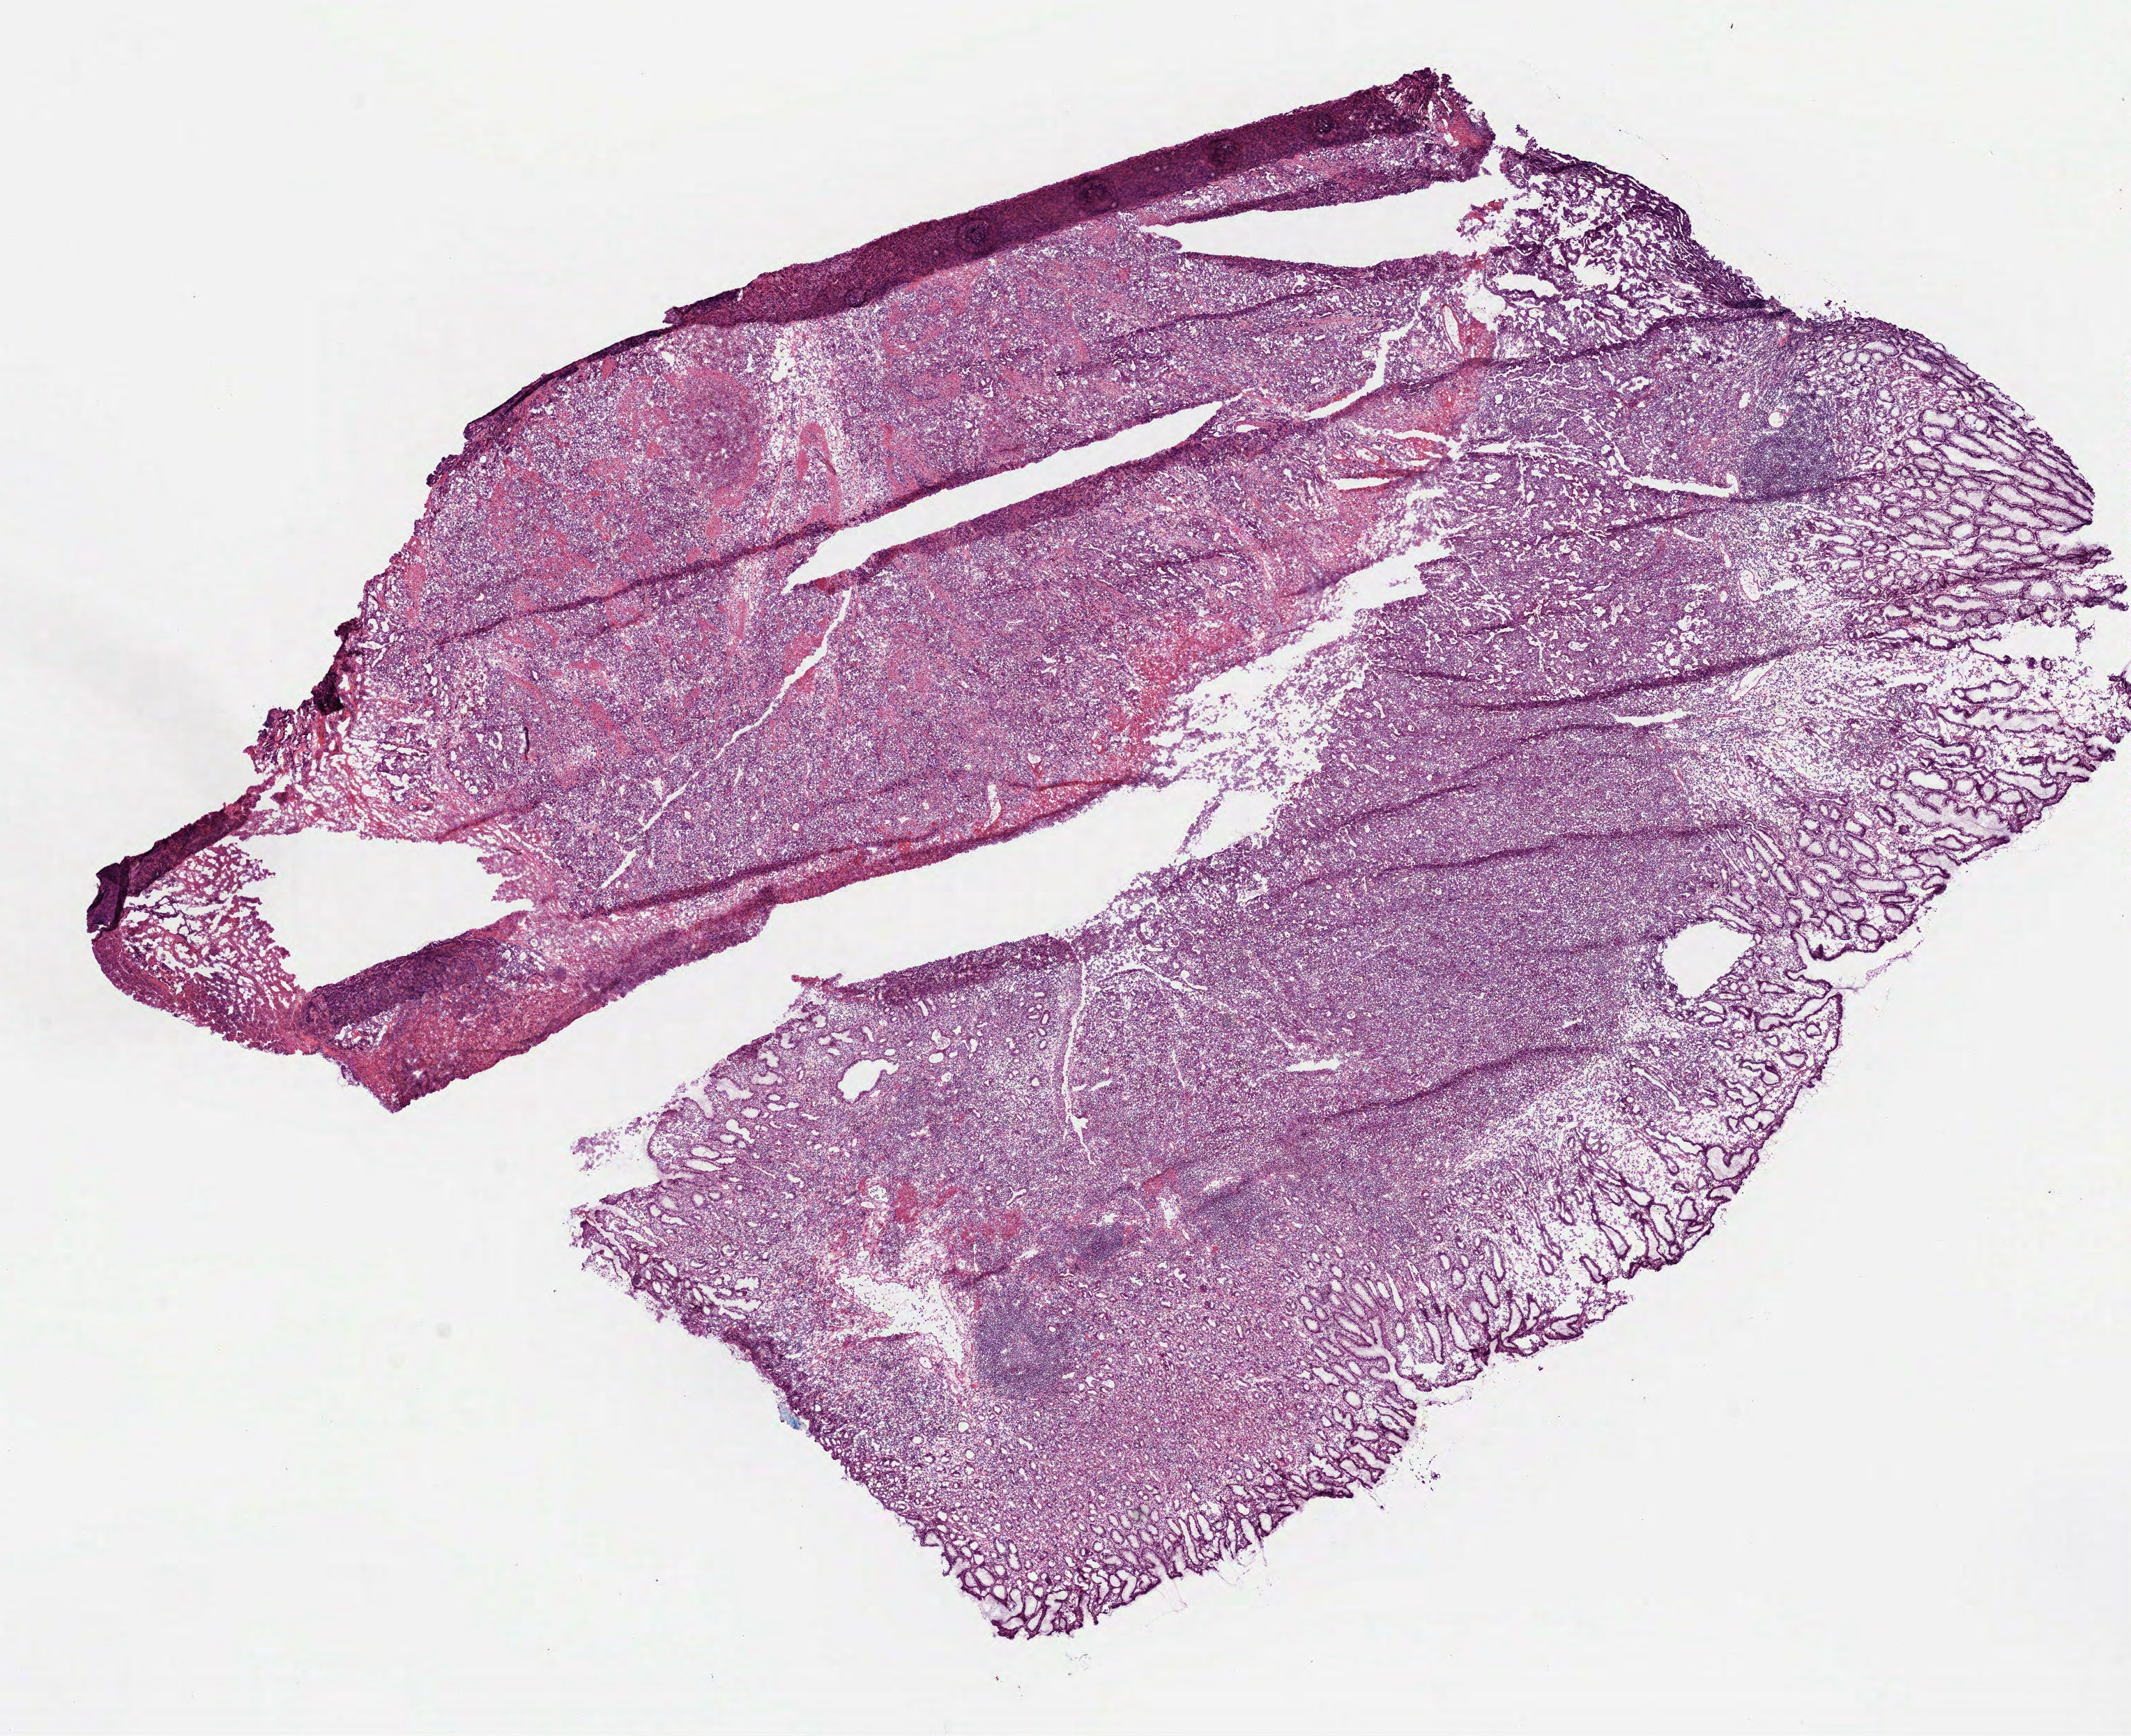
Whole-slide histology image, H&E-stained — a low-resolution overview of the entire scanned area, about 12.3 x 10.0 mm, frozen section, stomach, primary tumour sample. Patient: female, age at initial diagnosis 71 years.
Pathologic diagnosis: Signet ring cell carcinoma (body of stomach).